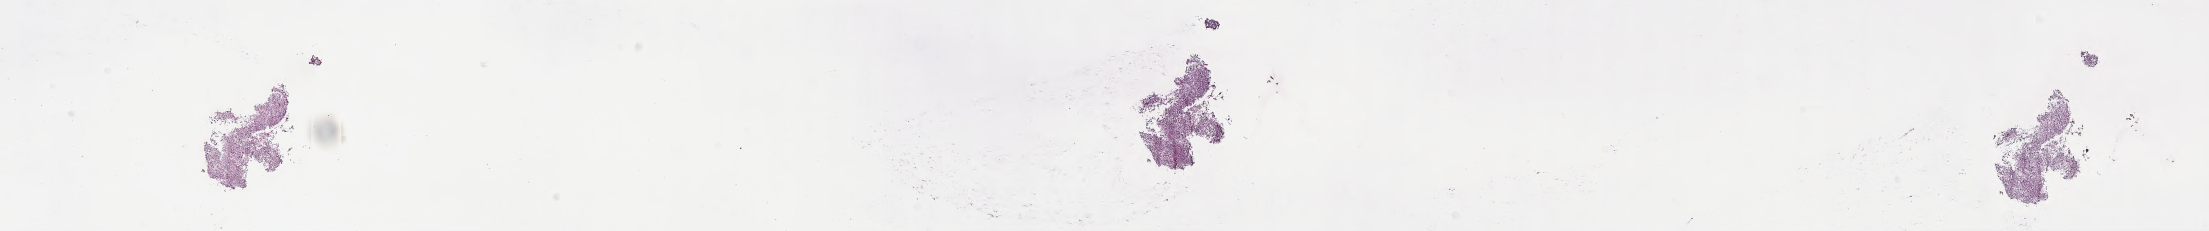
Digitized H&E-stained section of tumor tissue from the brain — low-resolution overview of the scanned area, about 35.7 x 3.7 mm, frozen section (OCT-embedded). Patient female; age 196 months (16 years 4 months).
Diagnosis: Pinealoma.